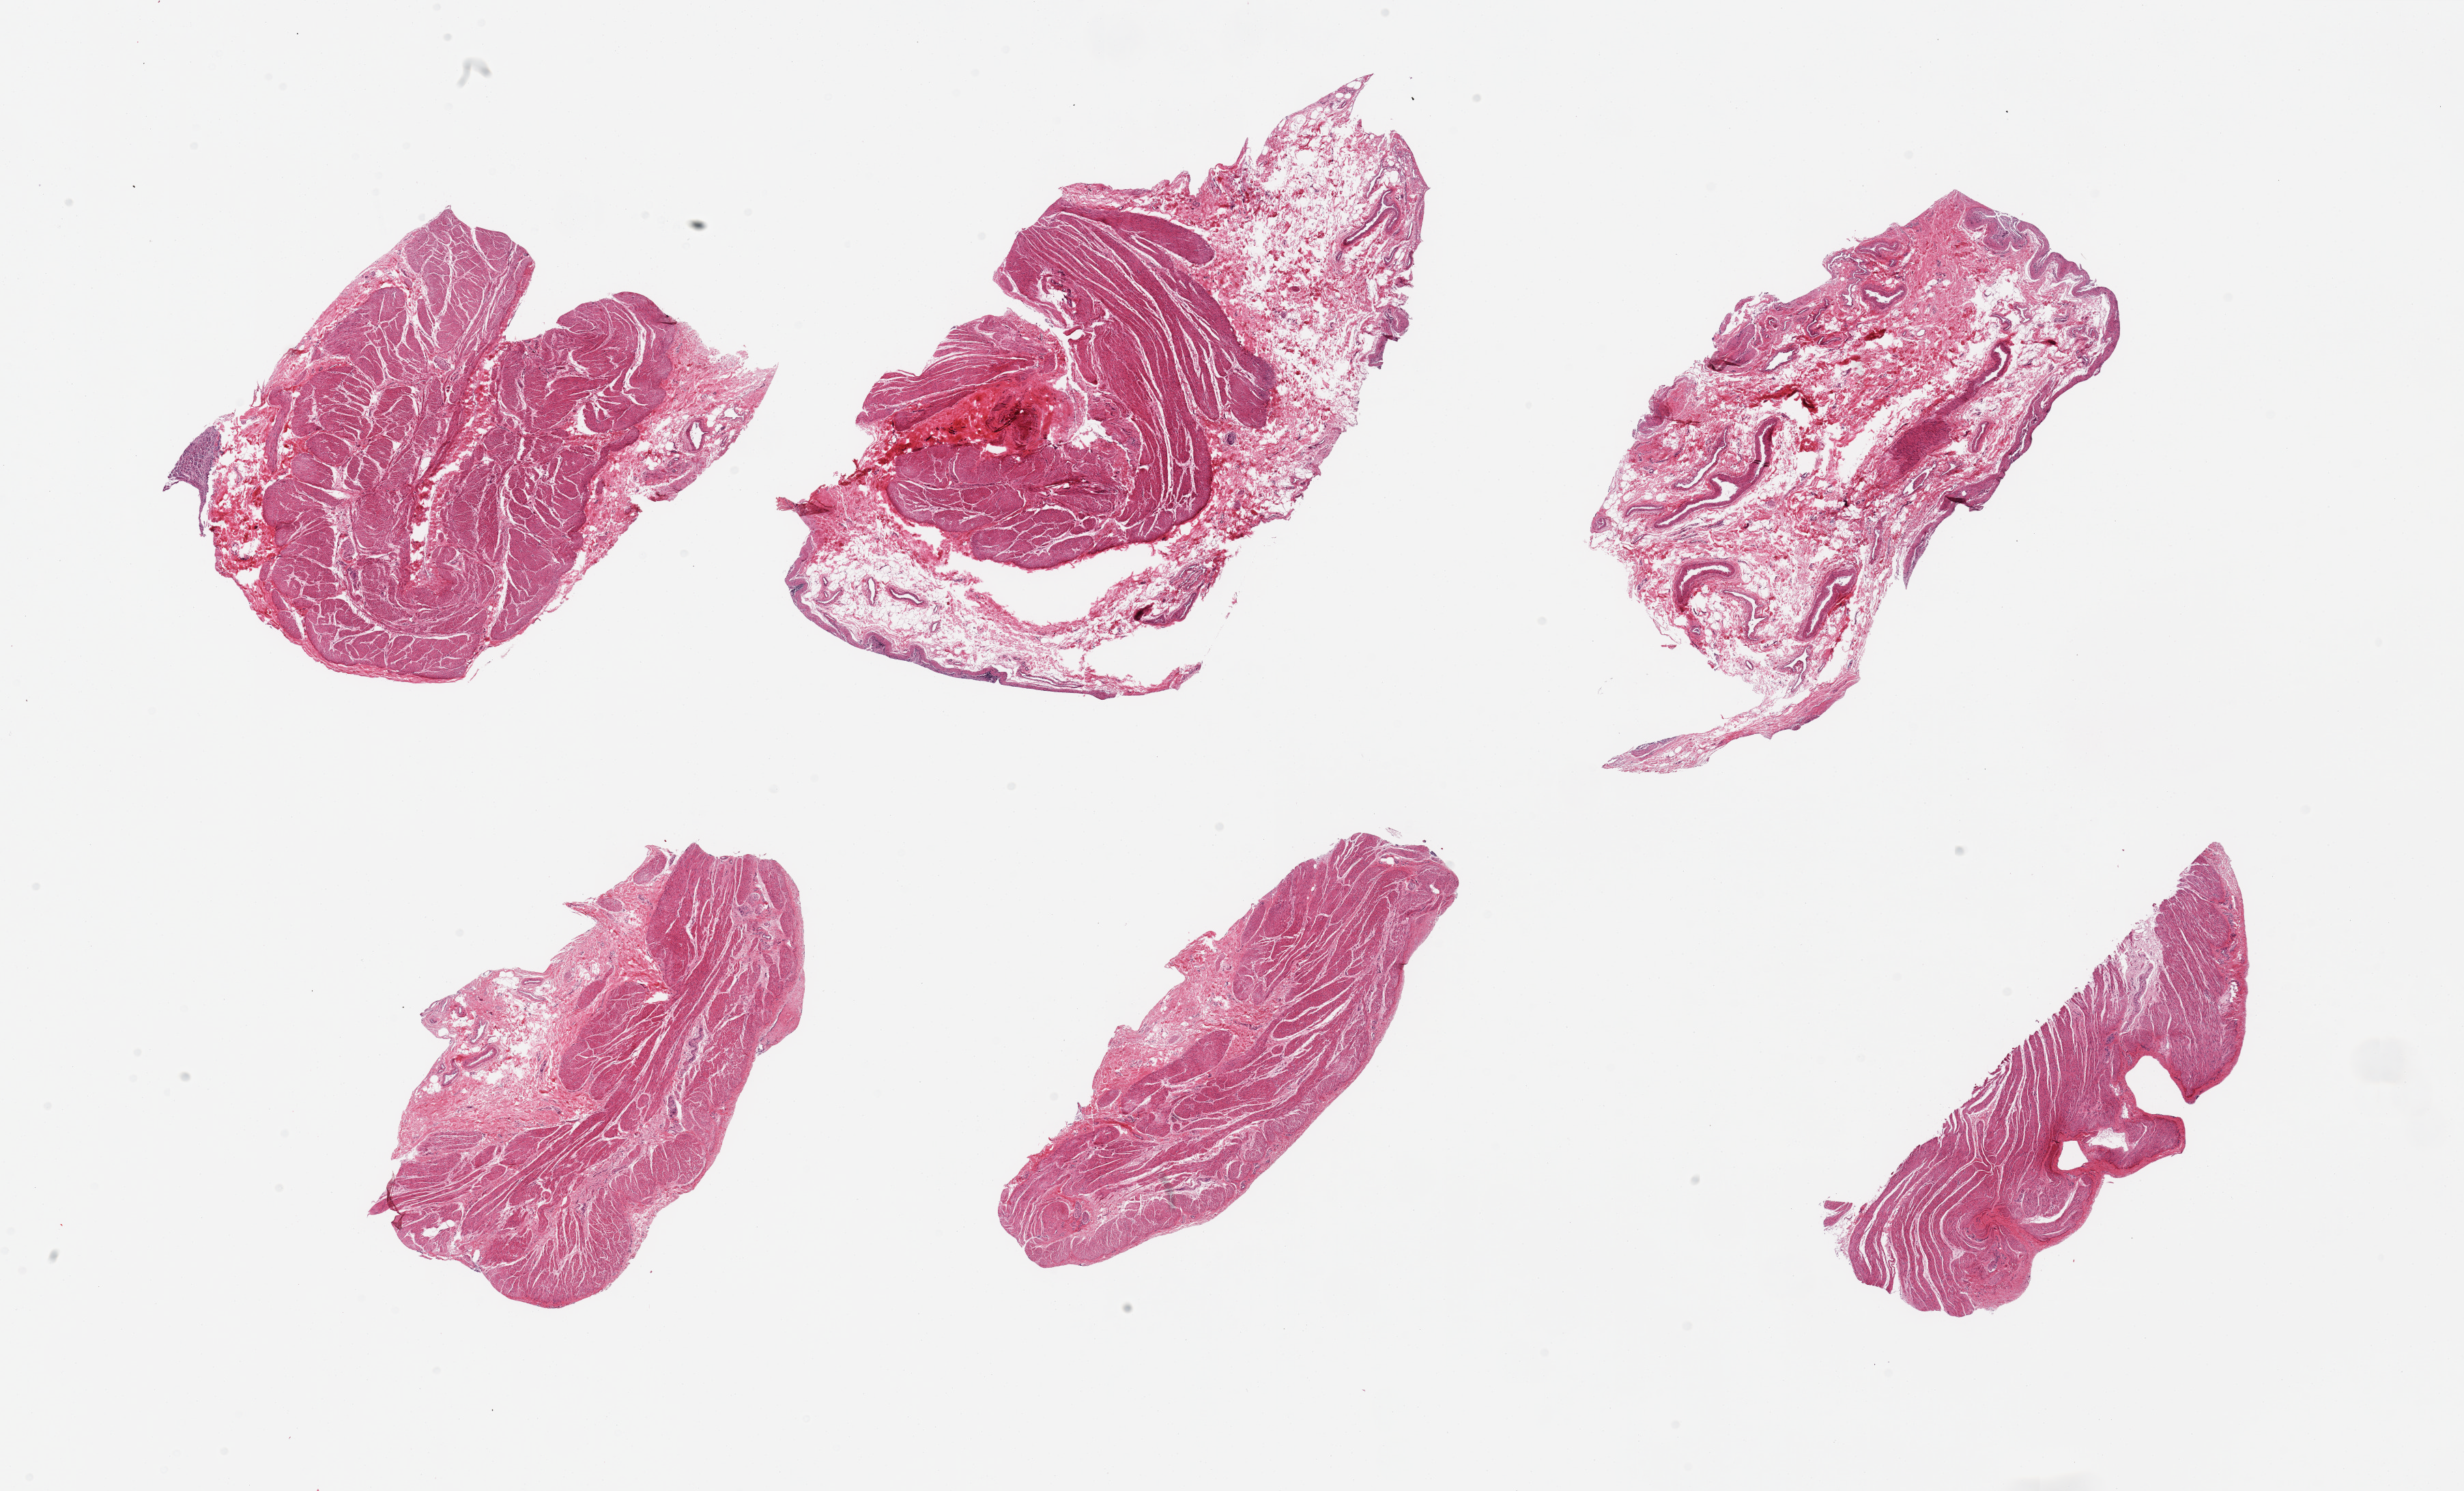
Whole-slide image, haematoxylin and eosin stain — low-resolution overview of the scanned area, about 28.5 x 17.3 mm (slide scanned at 20x). Donor sex: female.
Specimen: PAXgene-fixed paraffin-embedded (PFPE) section; sampled site (target tissue): stomach; tissue donor sample.